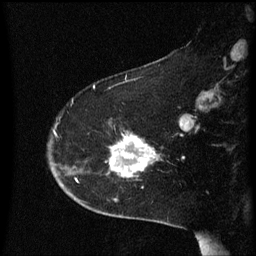
Breast MRI (dynamic contrast-enhanced), one sagittal slice. Dynamic contrast-enhanced series, image 2 of 3 at this slice position (ordered by acquisition). 1.5 T. TE 4.2 ms, TR 8.4 ms. 2 mm slice thickness. 256 × 256 image matrix, field of view 200 × 200 mm. Female patient, age 54 years. Case-level facts recorded for this patient, not image findings: setting: breast cancer imaged before/during neoadjuvant chemotherapy; receptor status: HR-positive, HER2-negative.
Structures marked on this image (semi-automatically segmented with operator editing):
- analysis volume of interest (the breast-tissue region the enhancement analysis was run in; not a lesion): bounding box (x1, y1, x2, y2) in pixels: (99, 132, 164, 189)
- tumour enhancement mask (voxels above the 70 % enhancement threshold inside the analysis volume of interest): (111, 136, 158, 179)